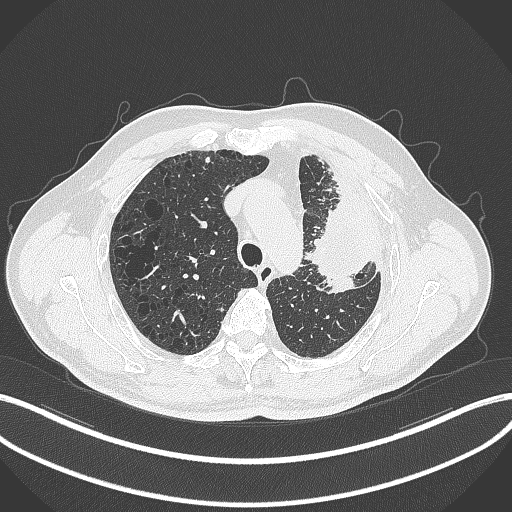
Chest CT, one axial slice. Position 241 of 297 along the scan axis. Lung window (W 1500 / L -600 HU). 1 mm slice thickness. 512 × 512 image matrix. Male patient, age 68 years. From the clinical record (not read from this slice): clinical TNM (as recorded): T3 N3 M1.
Structures marked on this image (rectangle marked by the reading radiologist):
- lung tumour (recorded histology: adenocarcinoma): box from (x=303, y=195) to (x=366, y=298) px